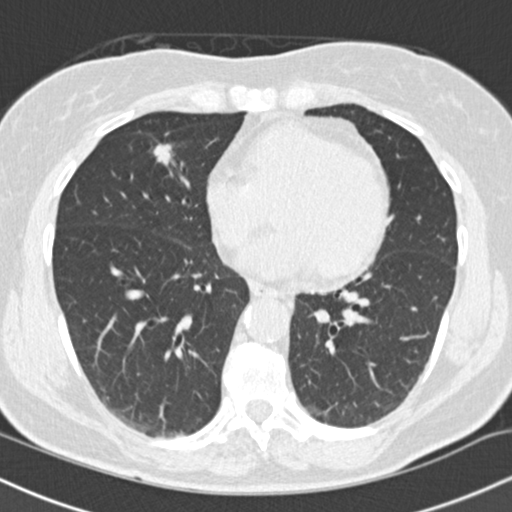
Low-dose screening chest CT, one axial slice; position 61 of 145 along the scan axis; lung window (W 1500 / L -600 HU); 2 mm slice thickness; 512 × 512 image matrix.
Structures marked on this image (expert manual segmentation):
- lesion 1 (tumor, middle lobe of right lung): box from (x=153, y=144) to (x=173, y=166) px